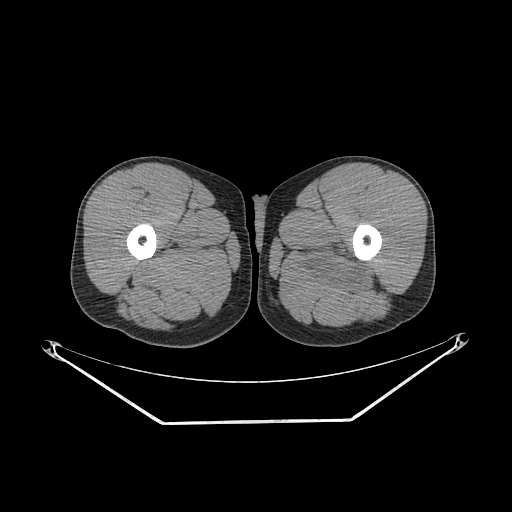
CT of an extremity soft-tissue mass (from a PET/CT study), one axial slice. Position 246 of 267 along the scan axis. Reconstruction kernel SOFT. 140 kVp. Soft-tissue window (W 400 / L 40 HU). 3.75 mm slice thickness. 512 × 512 image matrix, field of view 500 × 500 mm. Male patient. Case-level facts recorded for this patient, not image findings: histological type: extraskeletal osteosarcoma; grade: high; site of the primary tumour: left adductur.
Structures marked on this image (expert contour drawn on MRI and transferred to this co-registered scan by the dataset authors):
- gross tumour volume (mass): bounding box (x1, y1, x2, y2) in pixels: (290, 237, 378, 296)